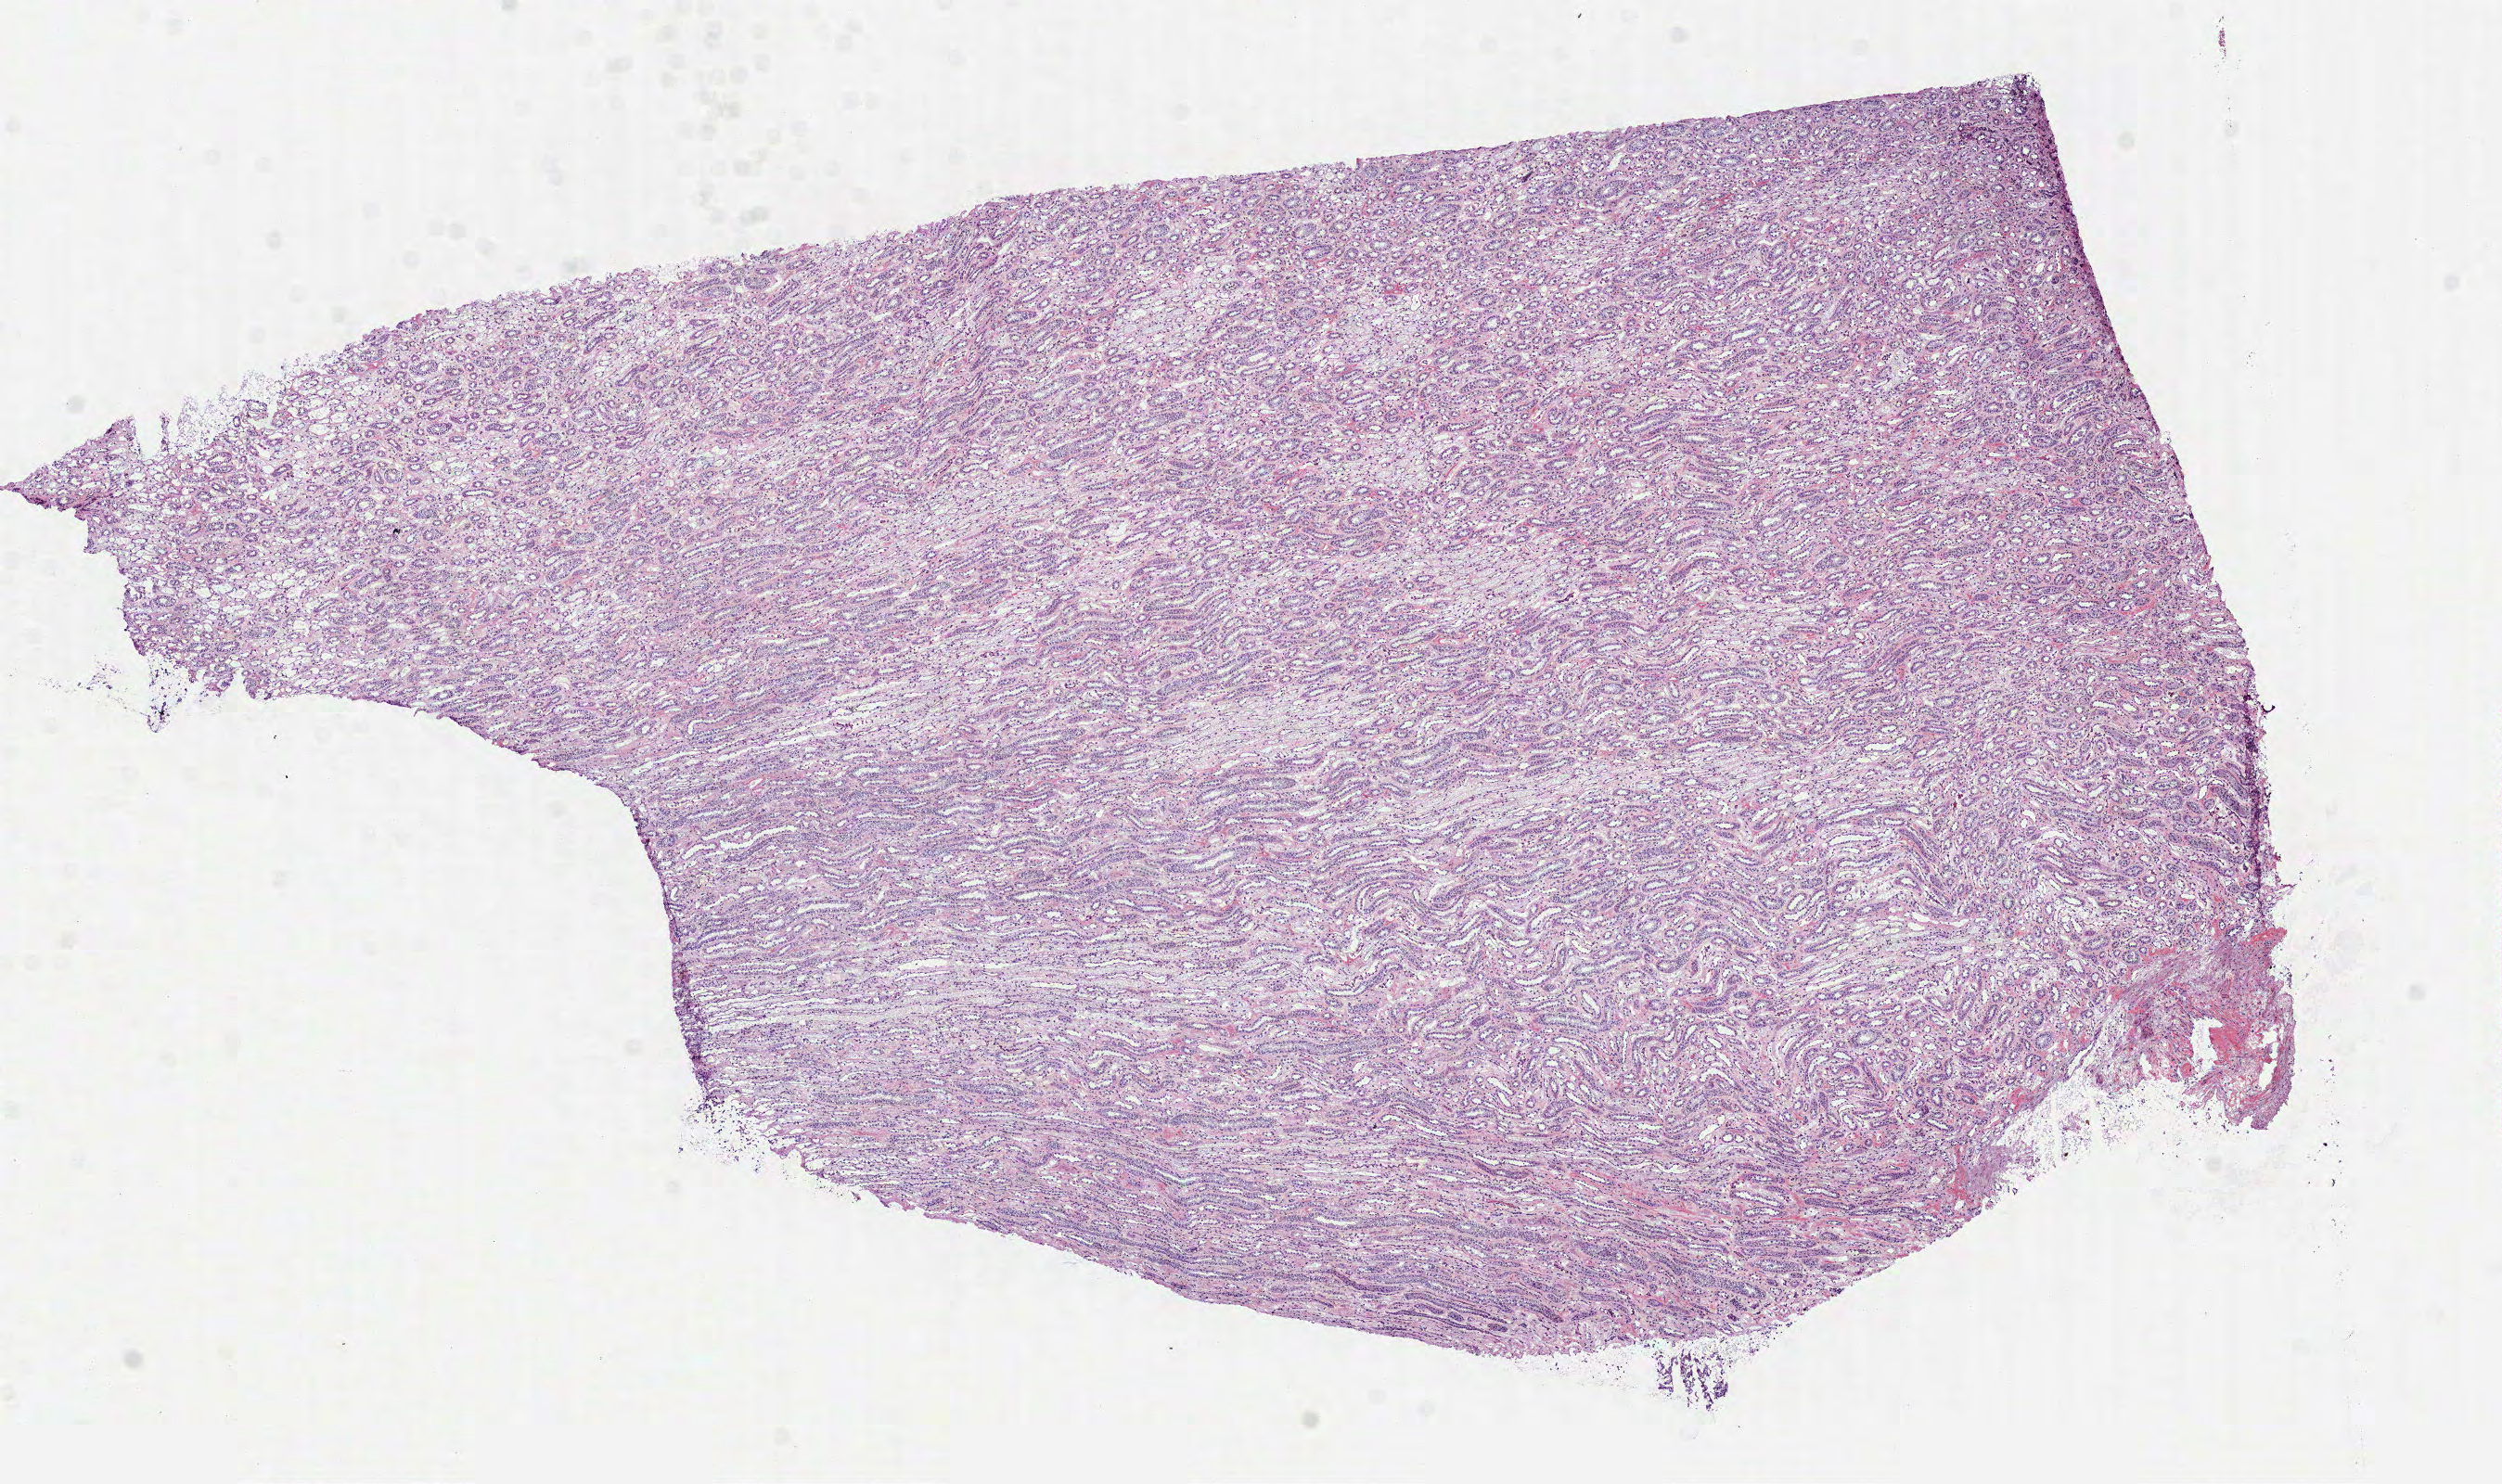
H&E whole-slide image — low-resolution overview of the scanned area, about 10.9 x 6.5 mm; frozen section from the top of the tissue portion; sample: solid tissue normal (non-tumour tissue), kidney. Patient: male, age at initial diagnosis 53 years.
* this section: solid tissue normal sample (biorepository sample class)
* patient diagnosis: Clear cell adenocarcinoma, NOS